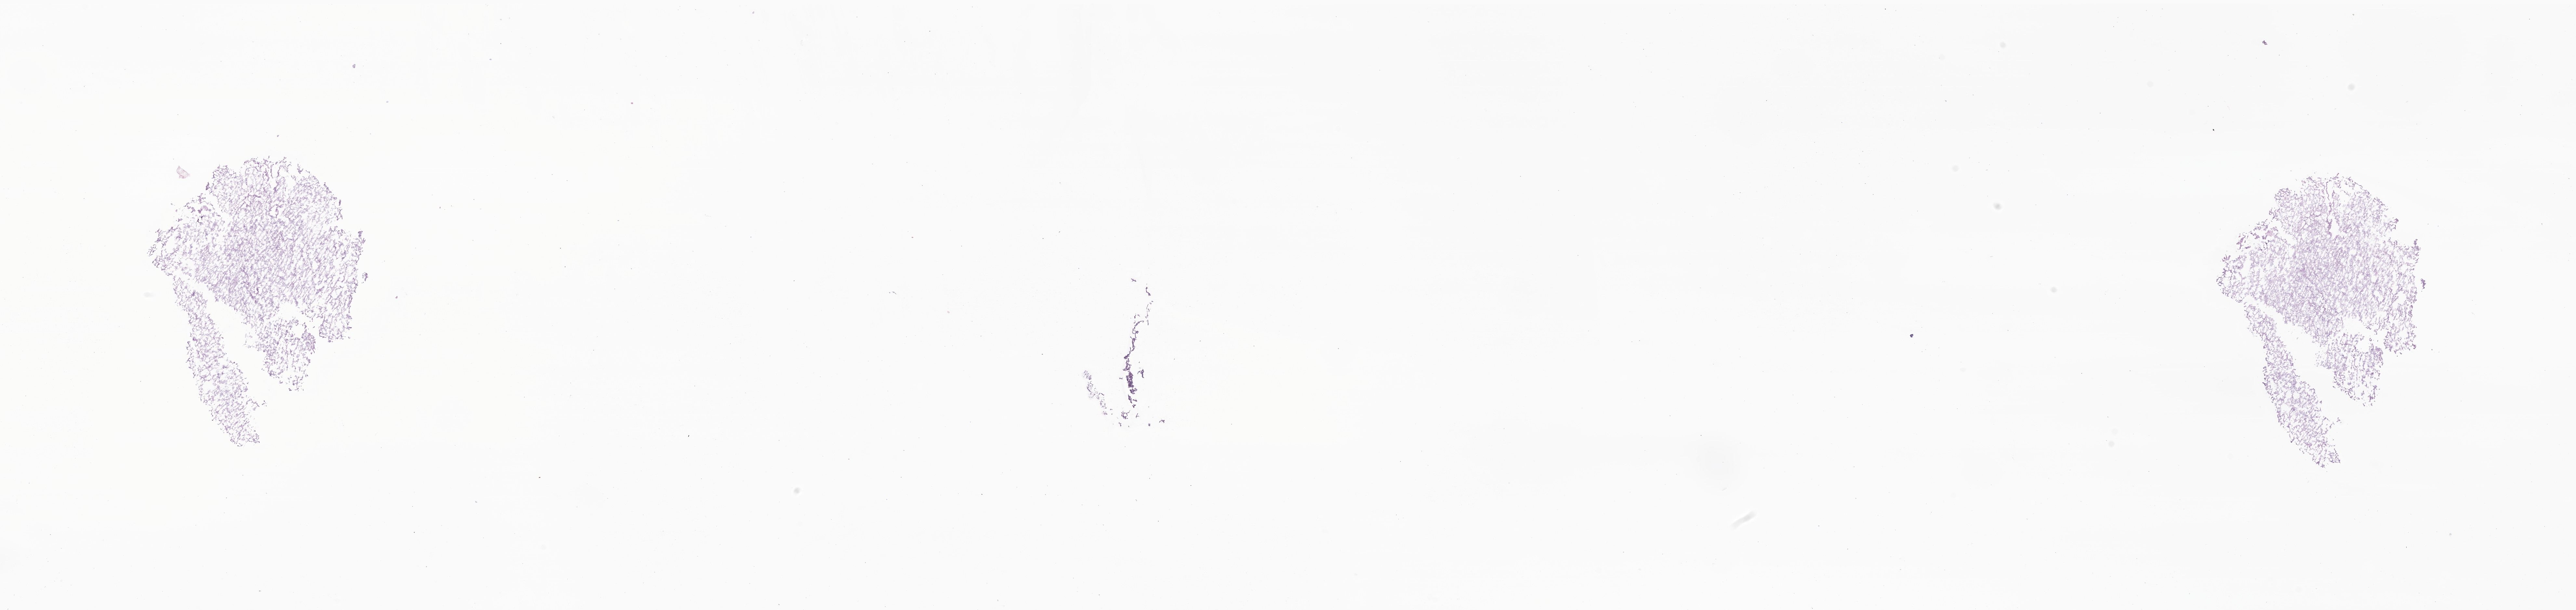
Whole-slide image, haematoxylin and eosin stain of tumor tissue from the brain, a low-resolution overview of the entire scanned area, about 33.2 x 7.9 mm. Frozen section (OCT-embedded). Male patient, age 58 months (4 years 10 months).
Recorded diagnosis: Pilocytic astrocytoma.